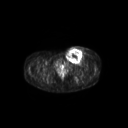
FDG PET of an extremity soft-tissue mass (from a PET/CT study), one axial slice. Position 62 of 267 along the scan axis. 3.27 mm slice thickness. 128 × 128 image matrix, field of view 600 × 600 mm. Patient: female, 24 years. From the clinical record (not read from this slice): histological type: leiomyosarcoma; grade: high; site of the primary tumour: groin.
Outlined on this slice (expert contour drawn on MRI and transferred to this co-registered scan by the dataset authors):
- gross tumour volume including surrounding oedema: bounding box <64,46,90,64> (left, top, right, bottom; pixels)
- gross tumour volume (mass): <65,47,83,64>